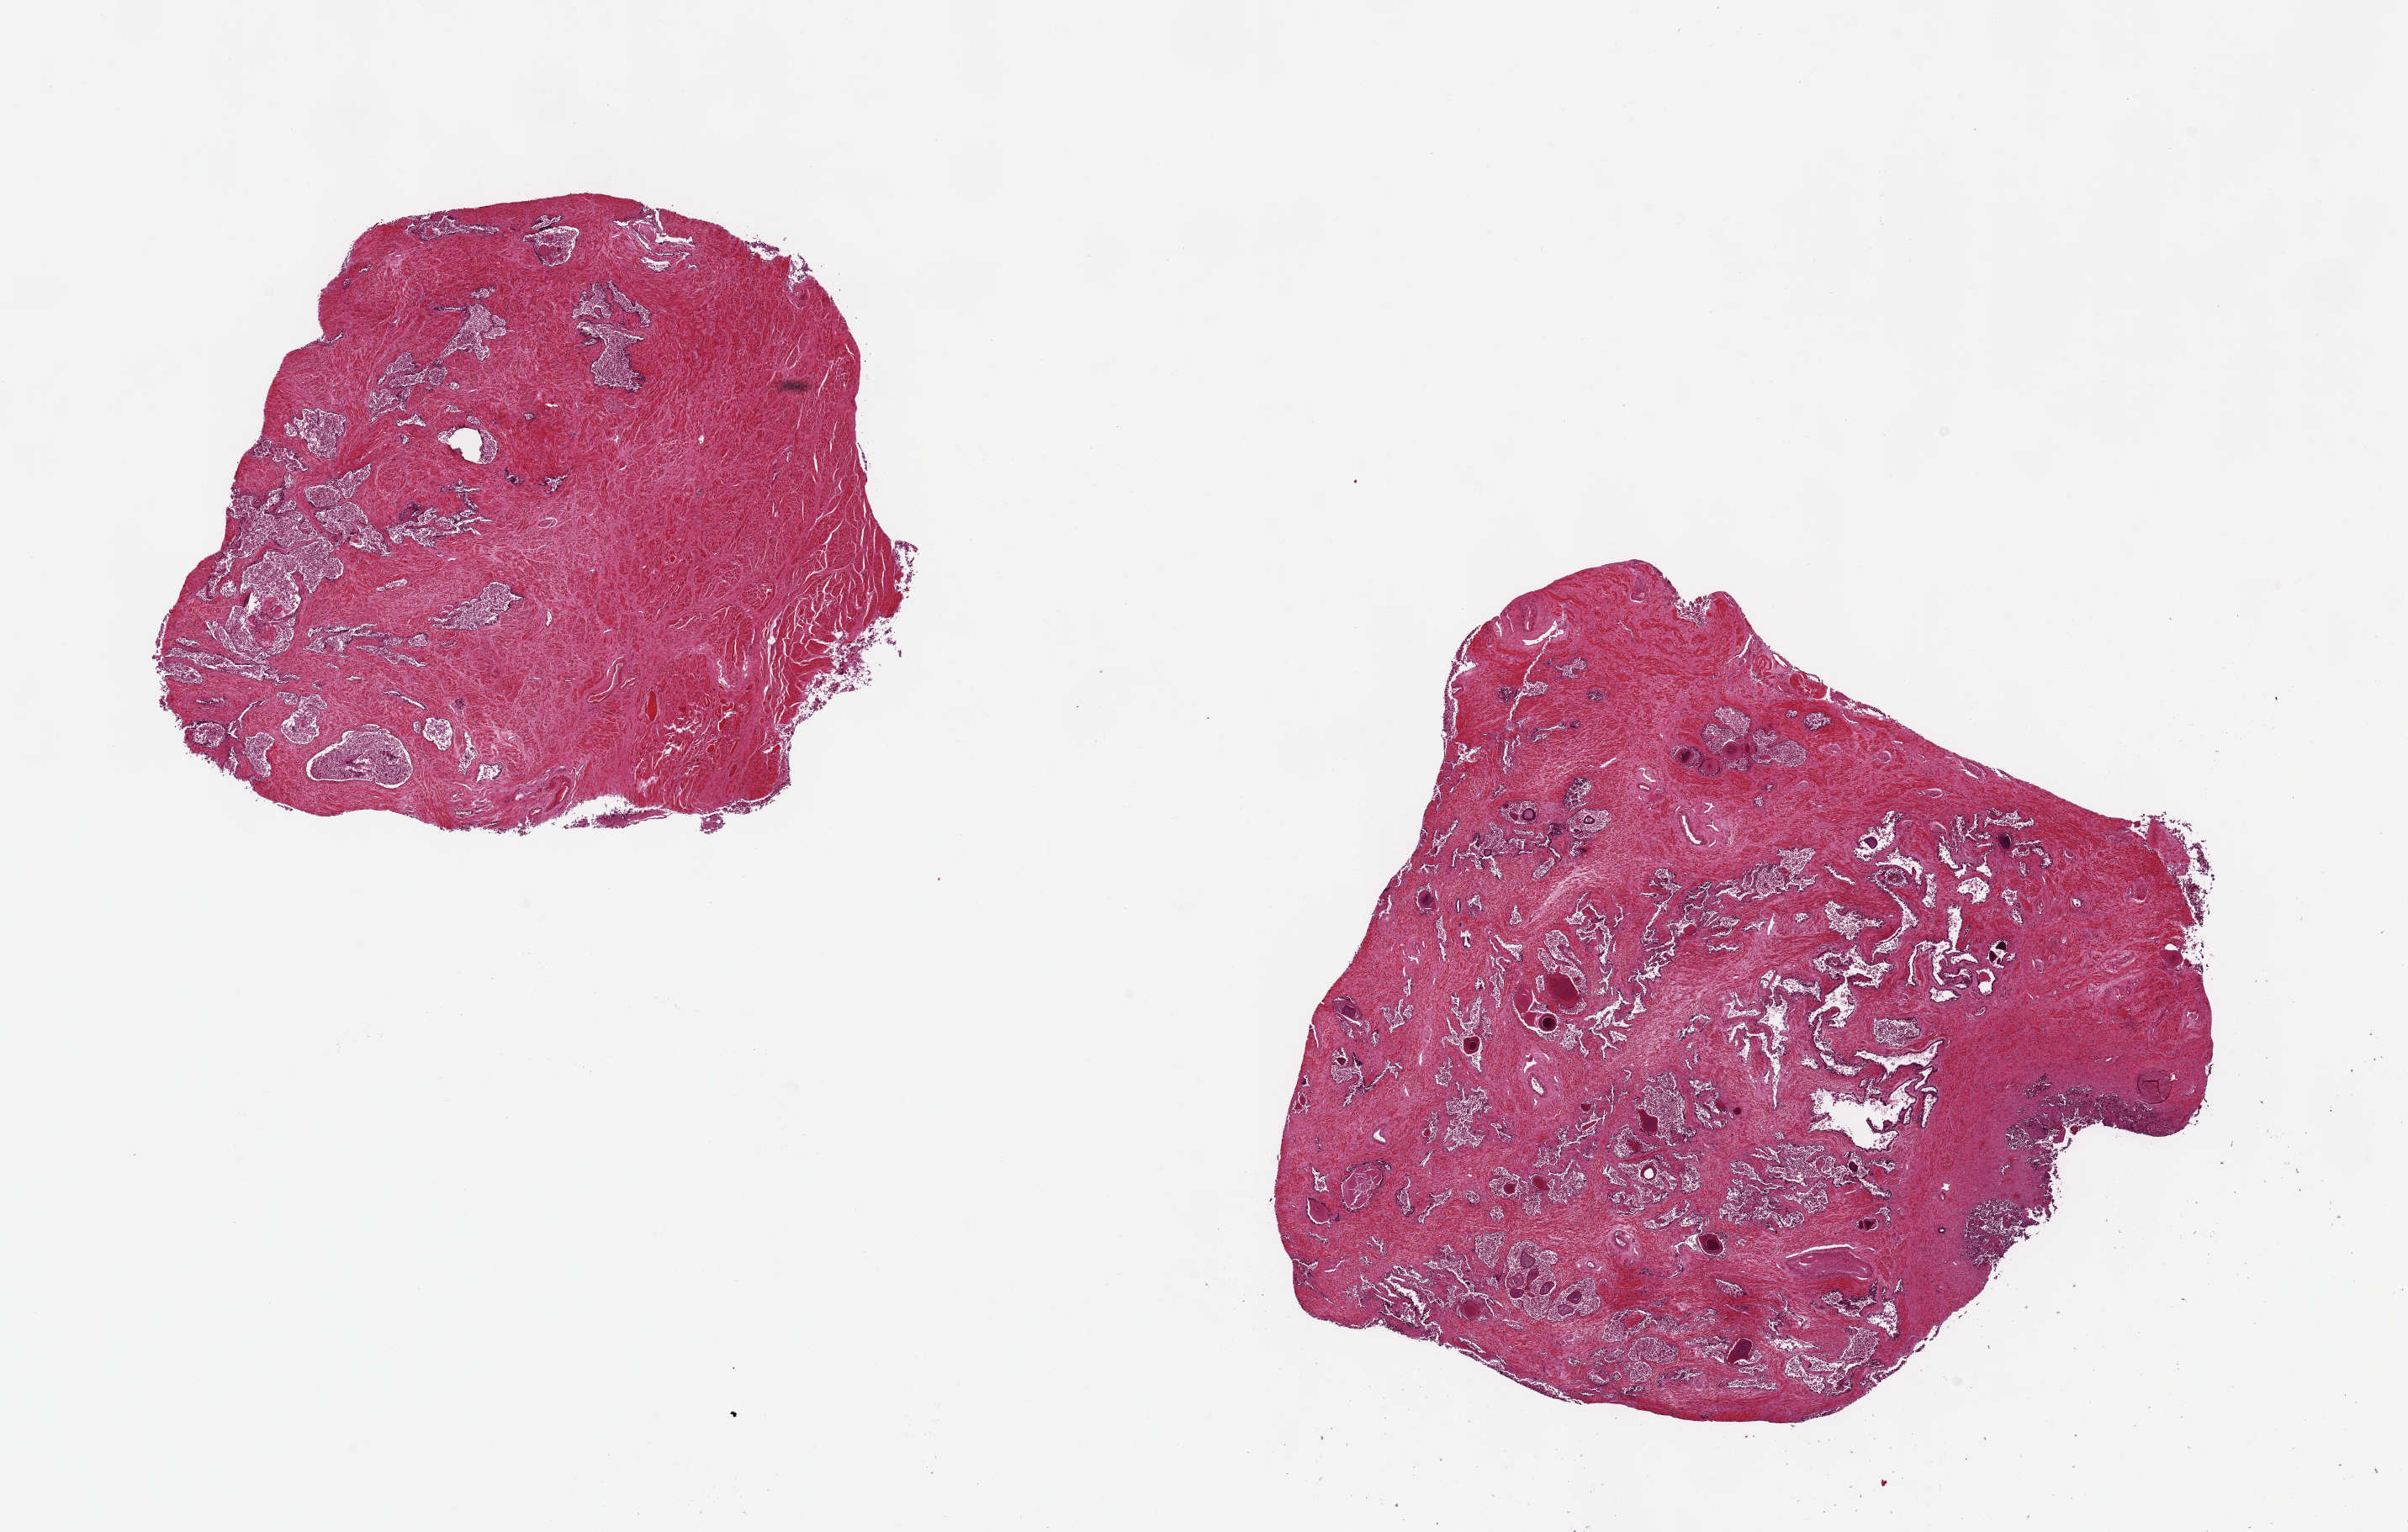
Digitized haematoxylin and eosin-stained section — whole scanned area (about 22.6 x 14.4 mm) shown as a low-resolution overview, PAXgene-fixed, paraffin-embedded tissue, target tissue: prostate, donor tissue sample. Donor: male.
Pathologist's review note for this sample: 2 aliquots, ~8x7mm. Glandular mucosa completely autolyzed.